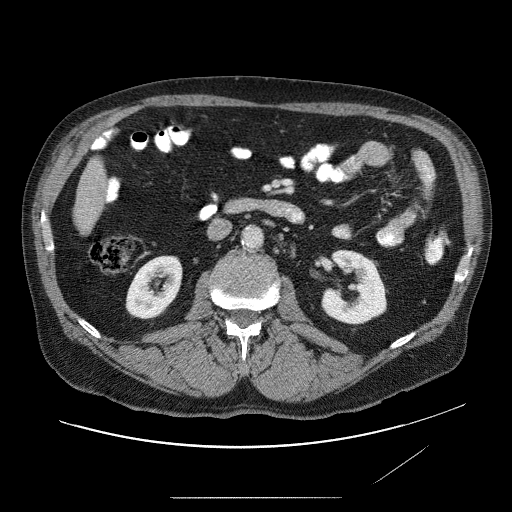
Contrast-enhanced abdominal CT (liver protocol), one axial slice; position 8 of 89 along the scan axis; reconstruction kernel STANDARD; soft-tissue window (W 400 / L 40 HU); 512 × 512 image matrix, field of view 420 × 420 mm. From the clinical record (not read from this slice): diagnosis: hepatocellular carcinoma (patient treated with transarterial chemoembolisation; whether this scan precedes or follows treatment is not stated here); TNM stage (as recorded): Stage-IVA; Child-Pugh class: A.
Structures marked on this image (semi-automatic segmentation, software-assisted and operator-edited):
- liver parenchyma outside the tumour (the mass and vessels are separate outlines, so this box may not span the whole liver): bounding box (x1, y1, x2, y2) in pixels: (70, 144, 114, 238)
- liver vessels: (89, 194, 92, 201)